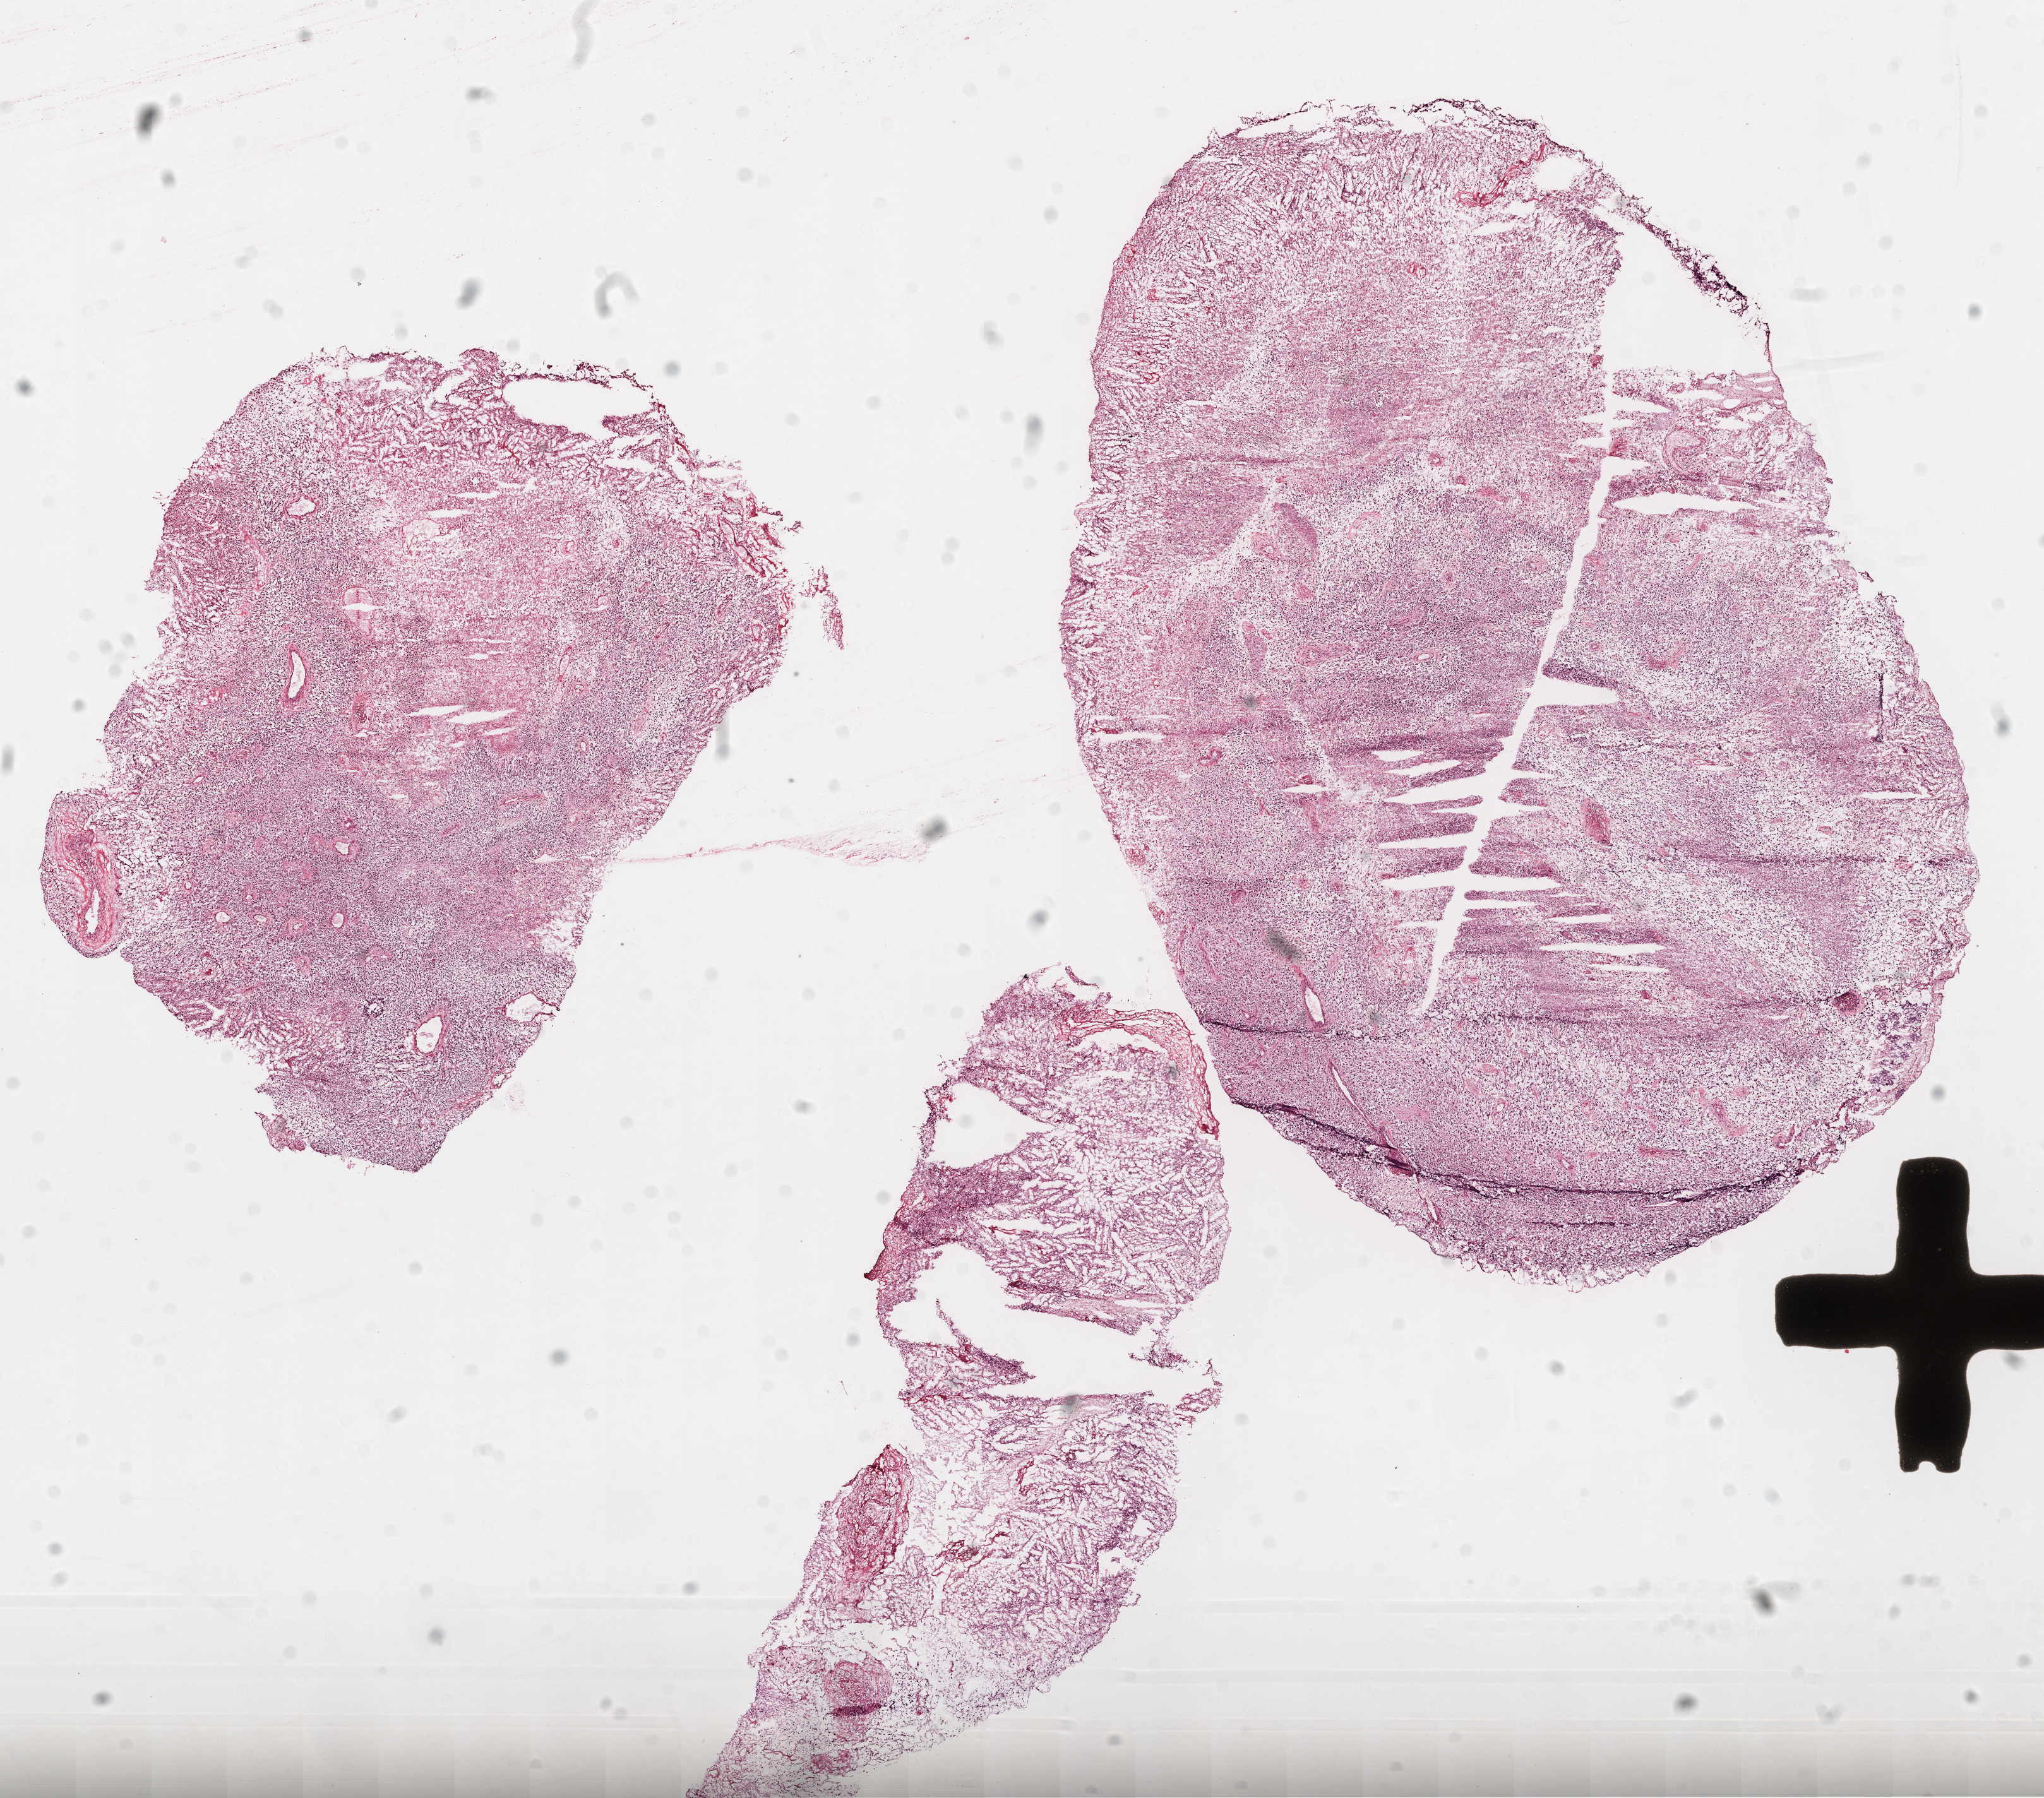
Whole-slide histology image, H&E-stained, shown as a low-resolution overview of the whole scanned area (about 13.1 x 11.5 mm), frozen section from the top of the tissue portion, brain, primary tumour sample. Patient: male, age at initial diagnosis 54 years. Pathologist review of this section (percent, as recorded): tumour cells 70%, tumour nuclei 95%.
Pathologic diagnosis: Glioblastoma.